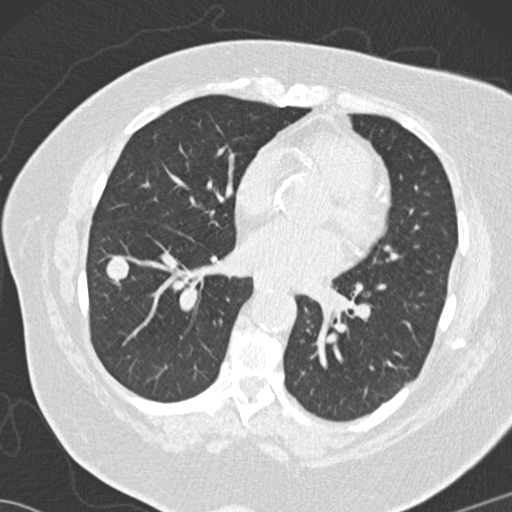
Low-dose screening chest CT, one axial slice; slice 62 of 146 in the series (ordered by position); reconstruction kernel B30f; lung window (W 1500 / L -600 HU); 2 mm slice thickness; 512 × 512 image matrix, field of view 350 × 350 mm.
Structures marked on this image (outlined manually by an expert reader):
- lesion 2 (tumor, lower lobe of right lung): bounding box (x1, y1, x2, y2) in pixels: (106, 257, 129, 280)